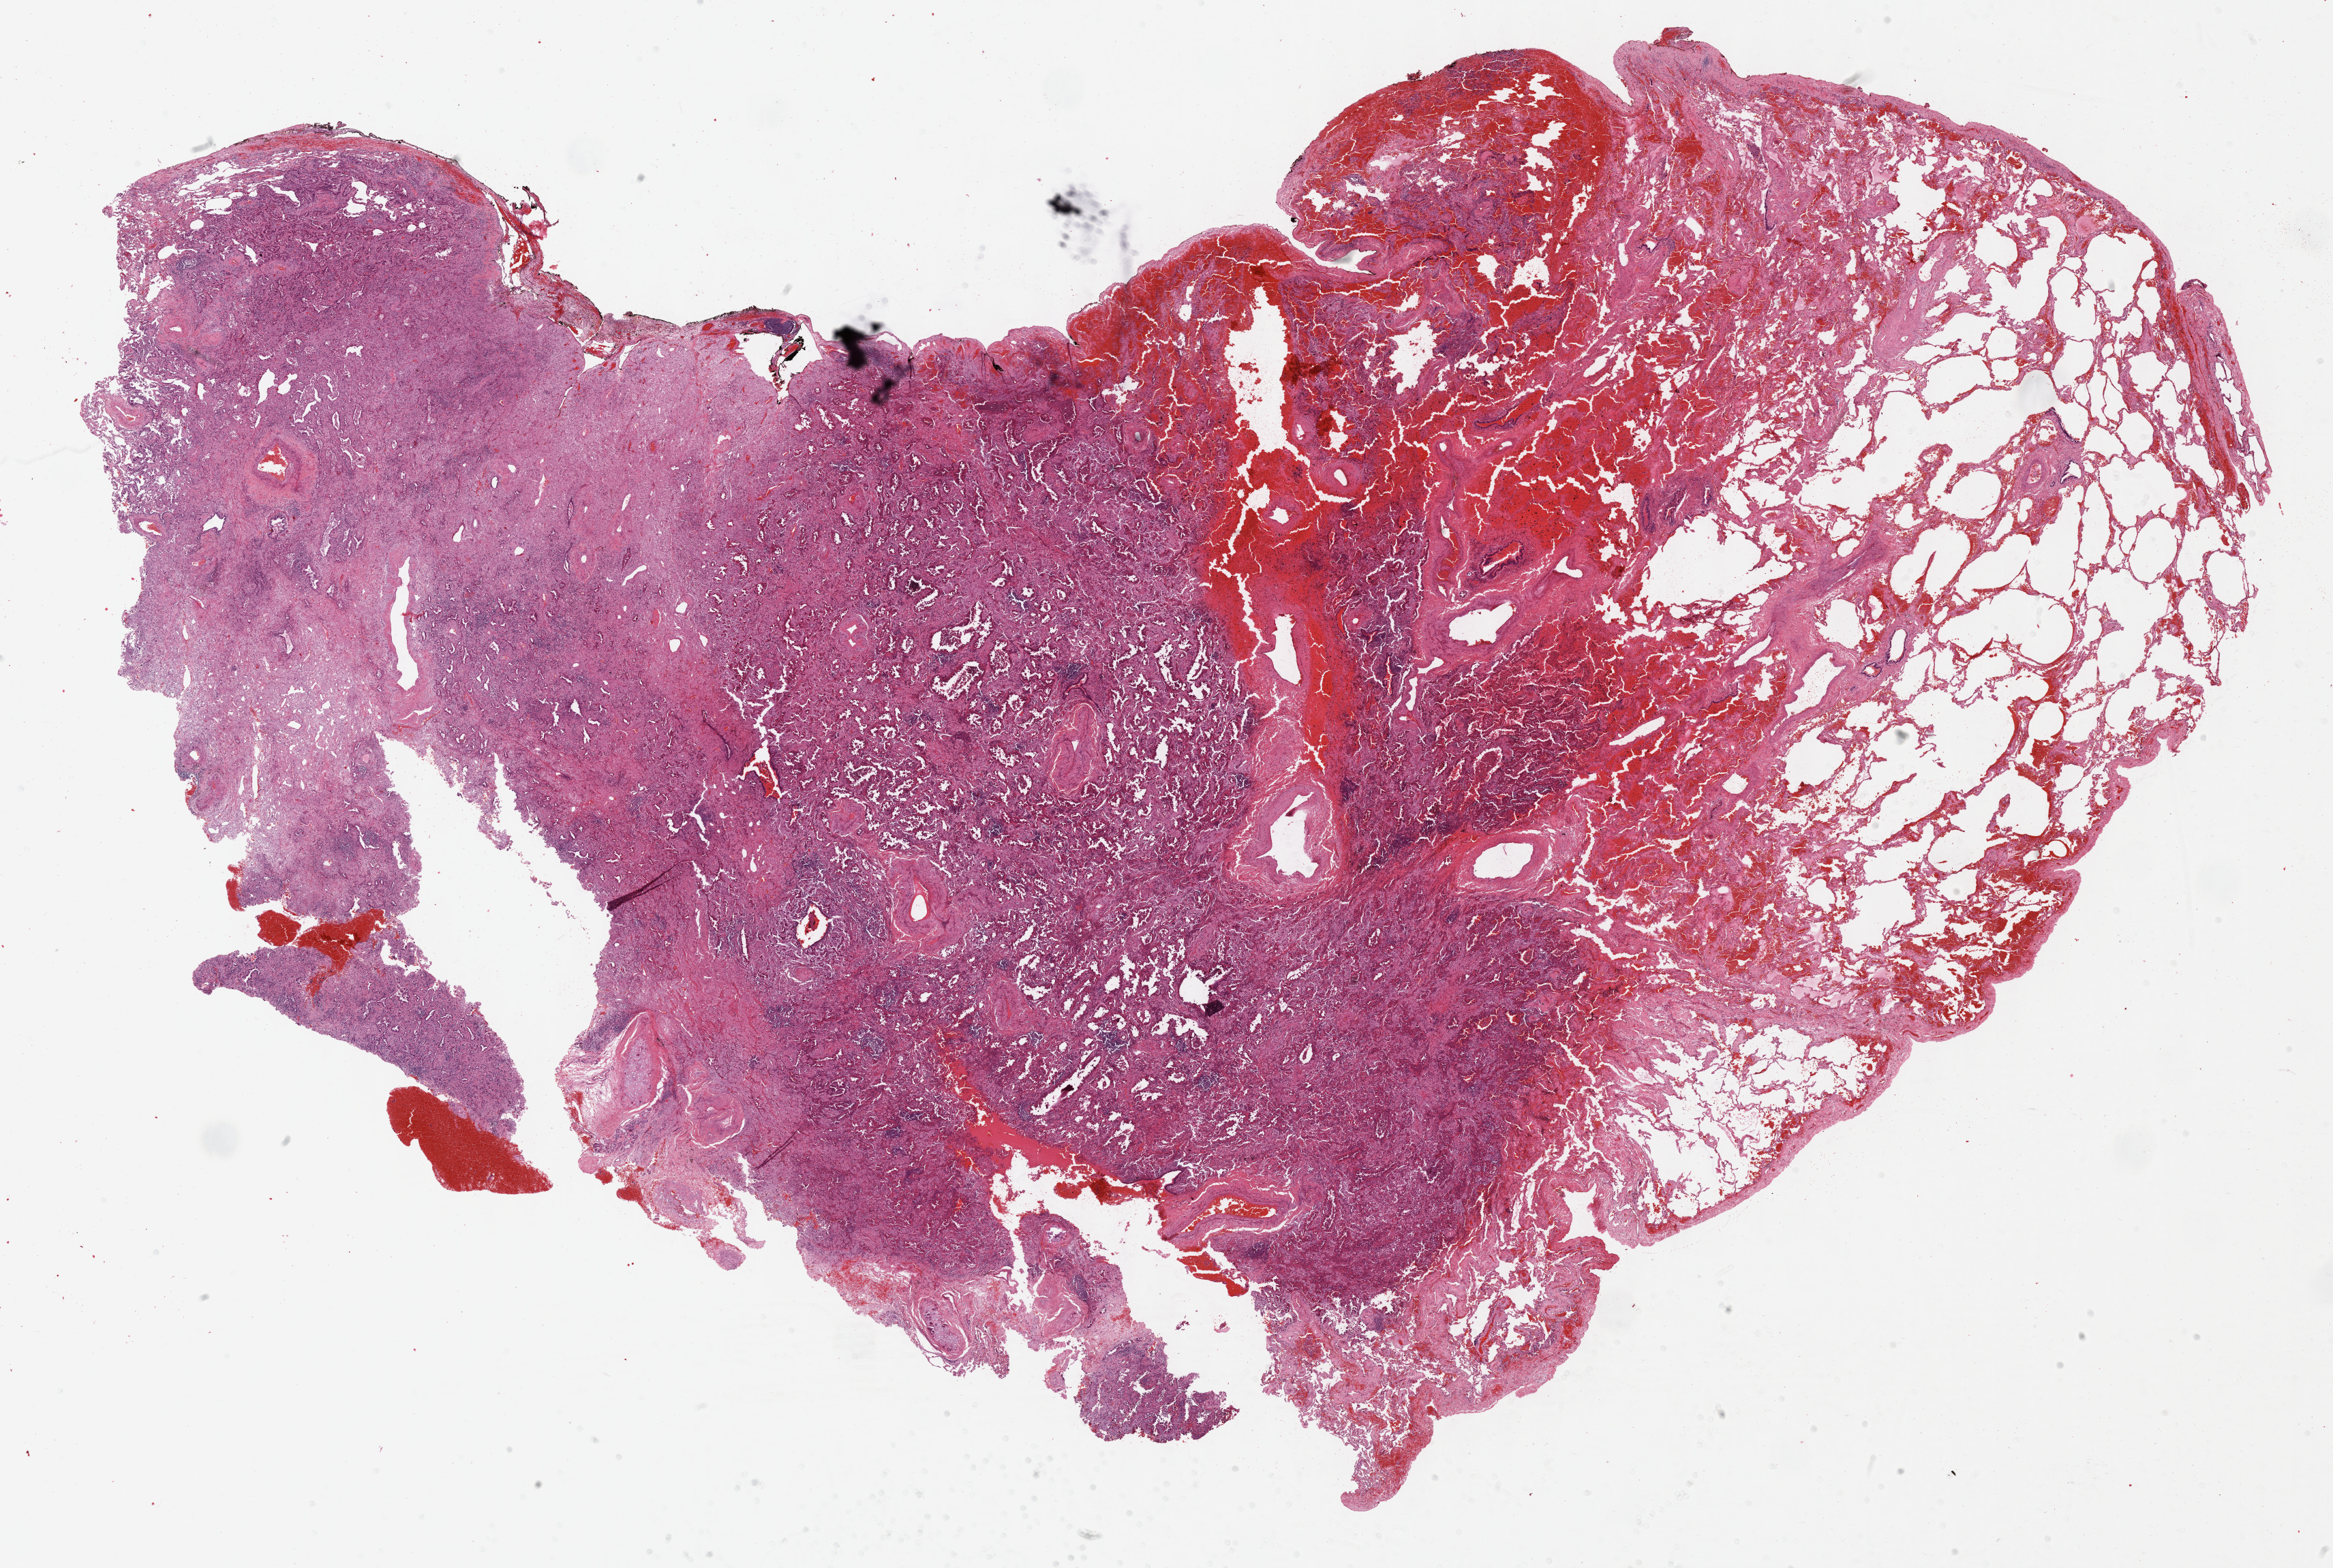
H&E whole-slide image, shown as a low-resolution overview of the whole scanned area (about 27.7 x 18.6 mm); formalin-fixed paraffin-embedded (FFPE) diagnostic section; liver, primary tumour sample. Male patient; age at initial diagnosis 61 years. Histologic grade: G2 (moderately differentiated).
- diagnosis: Combined hepatocellular carcinoma and cholangiocarcinoma
- AJCC pathologic stage: II (7th edition)